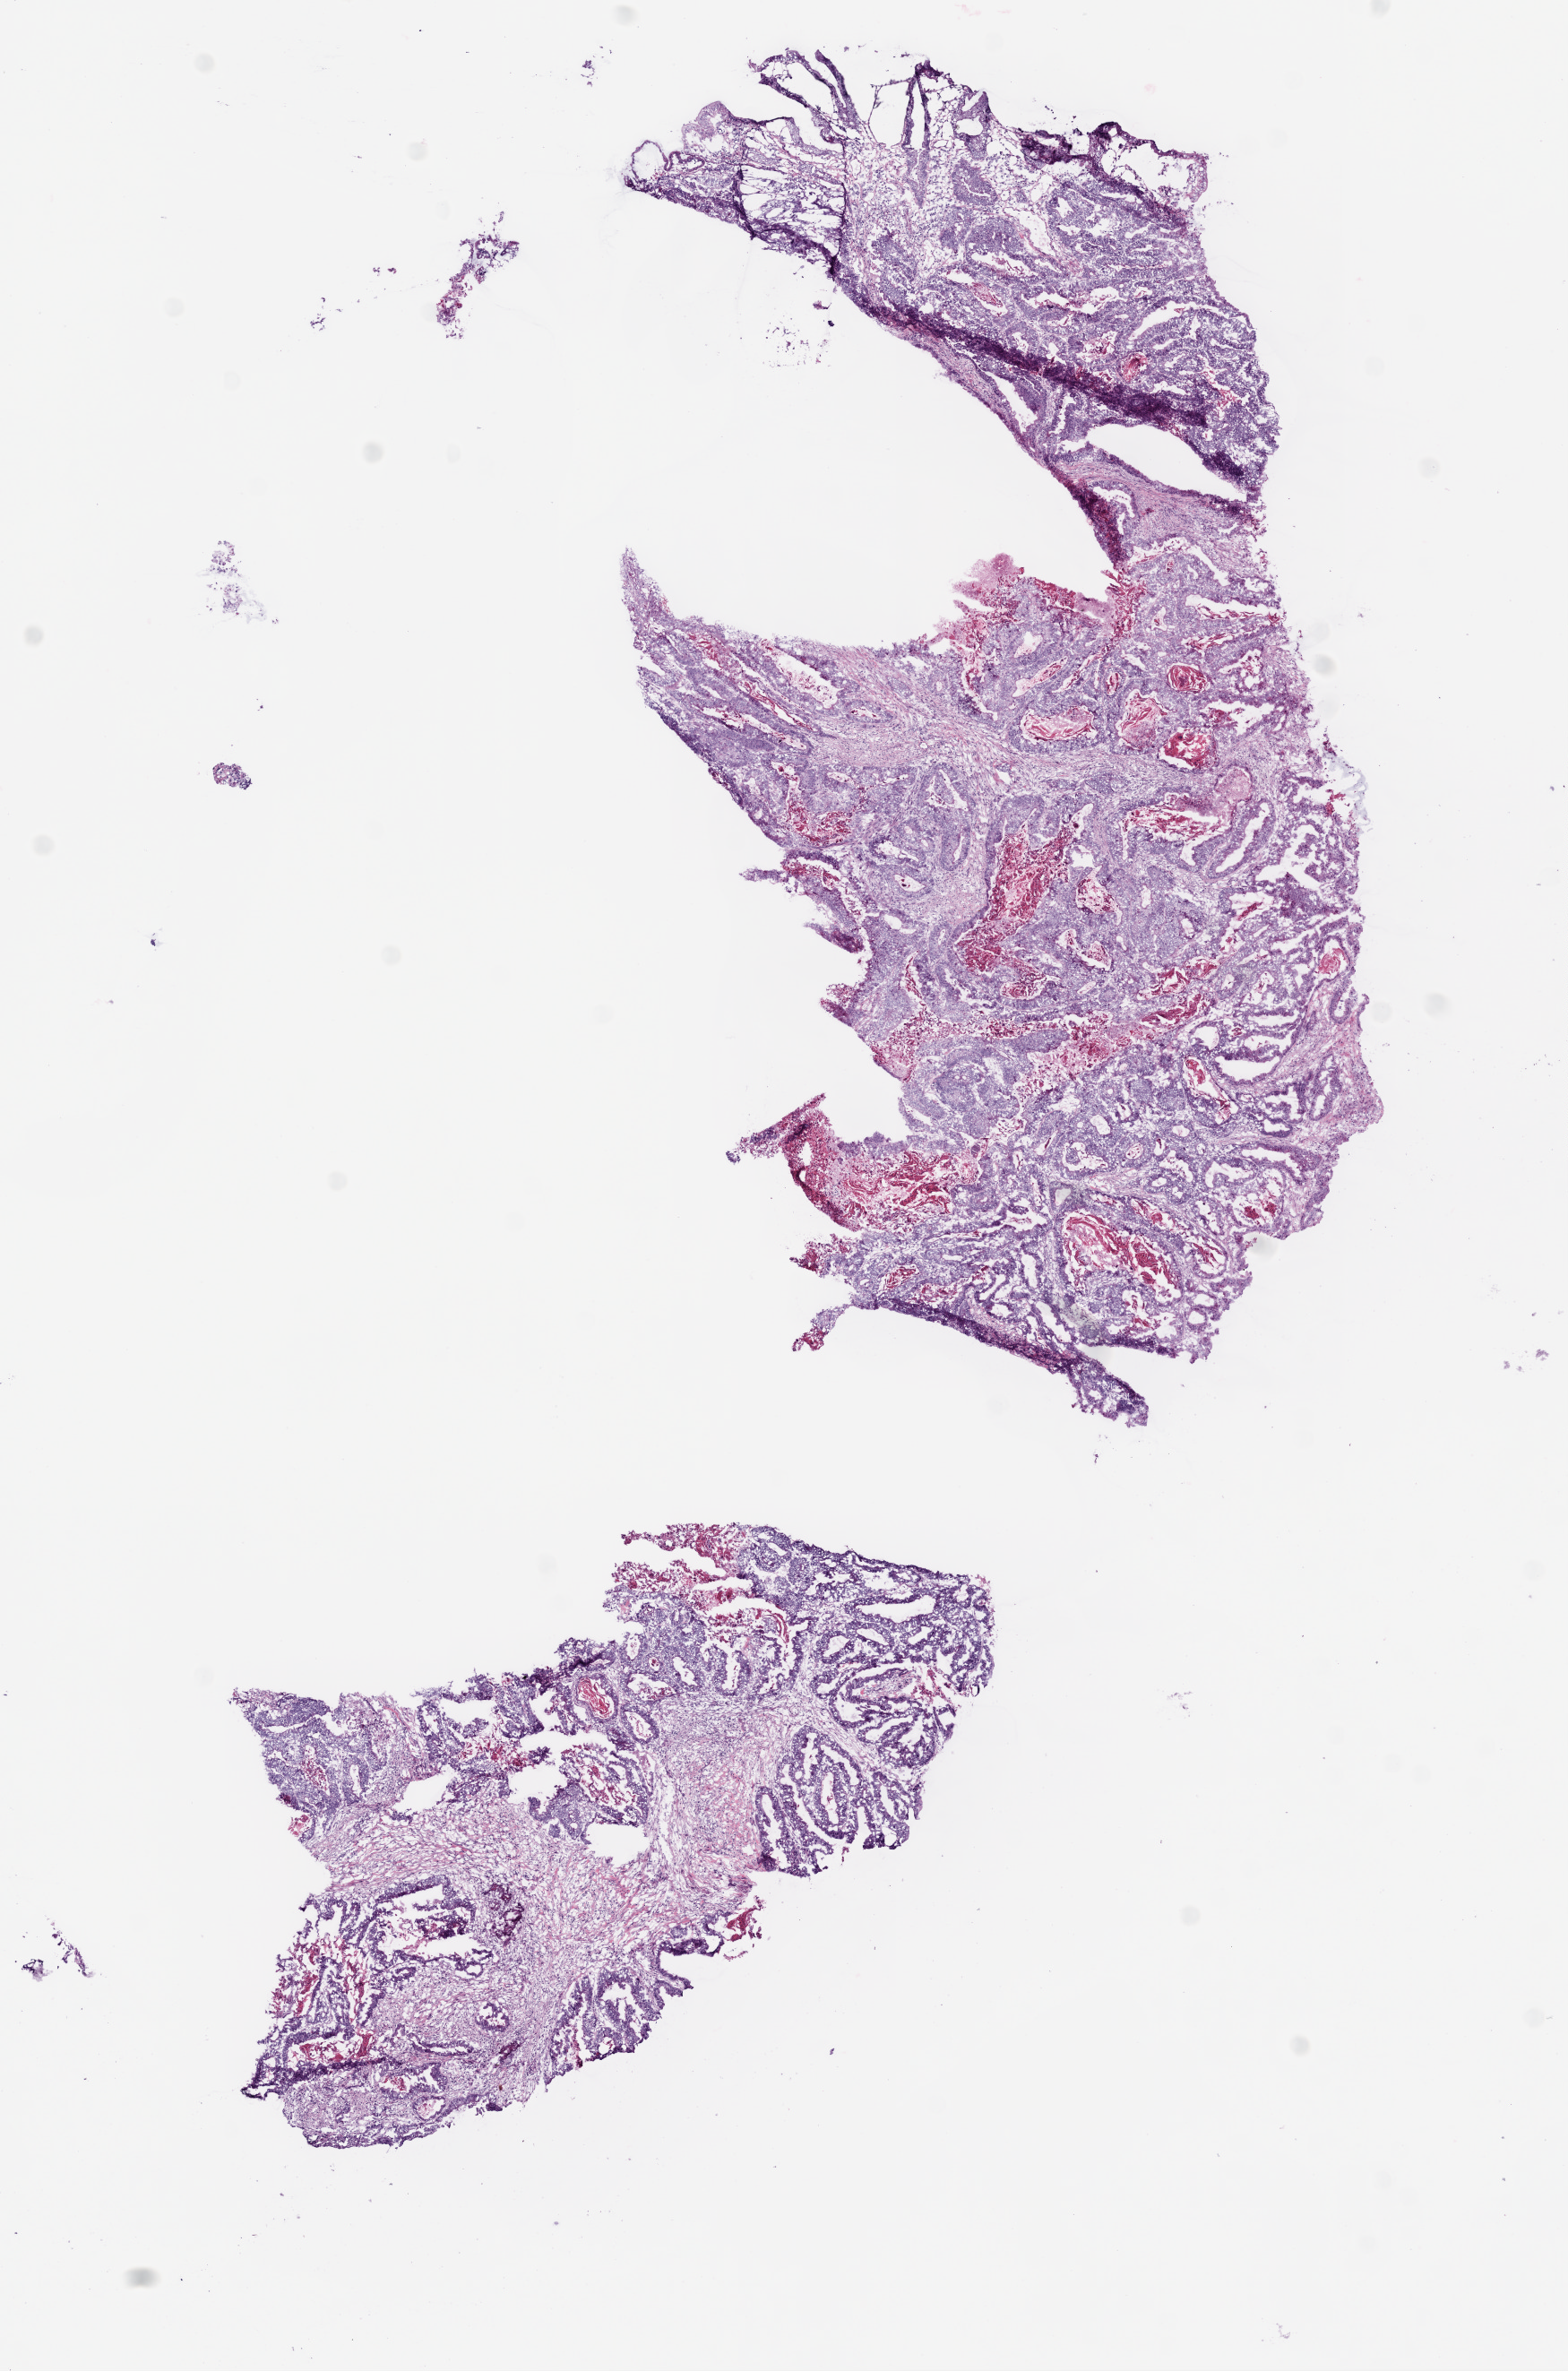
H&E-stained whole-slide image — low-resolution overview of the scanned area, about 7.0 x 10.6 mm (slide scanned at 20x). Frozen section from the bottom of the tissue portion. Sample: primary tumour, rectum. Female patient; age at initial diagnosis 65 years. Pathologist review of this section (percent, as recorded): tumour cells 65%, tumour nuclei 79%, normal cells 5%, stromal cells 30%, necrosis 0%.
AJCC pathologic stage: IIIC (6th edition). Diagnosis: Adenocarcinoma, NOS.